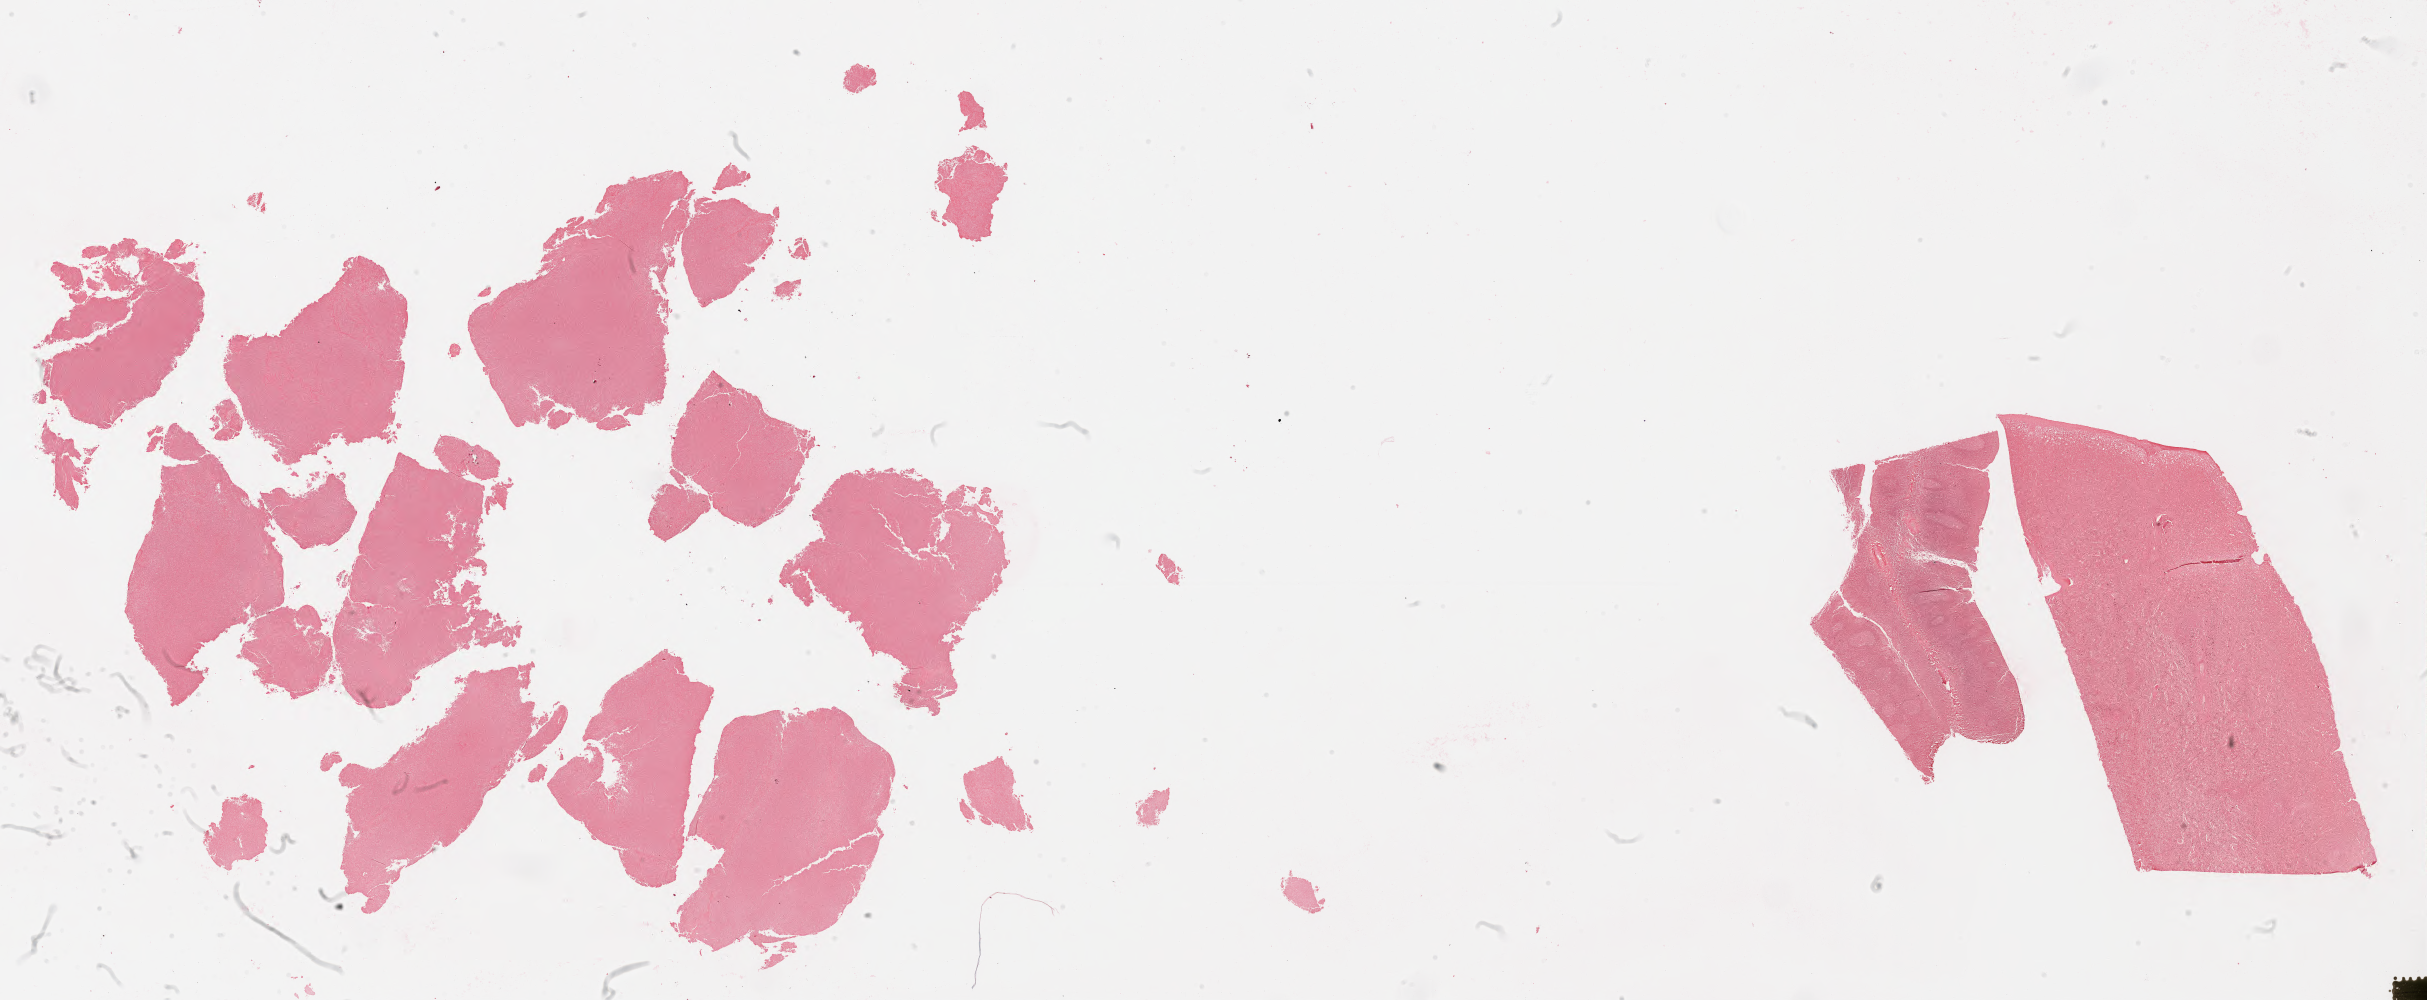
In-situ hybridisation whole-slide image, Epstein–Barr virus-encoded RNA (EBER) probe — low-resolution overview of the scanned area, about 39.2 x 16.2 mm. Tumor tissue. Site: lymph node. Patient female; aged 50.
Diagnosis: Diffuse large B-cell lymphoma, NOS.